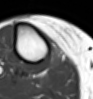
MRI of an extremity soft-tissue mass, one axial slice; MR volume resampled by the dataset authors to the PET/CT grid (not the native acquisition matrix); 3.27 mm slice thickness; 93 × 99 image matrix, field of view 91 × 97 mm. Female patient. Case-level facts recorded for this patient, not image findings: histological type: undifferentiated – high grade; grade: high; site of the primary tumour: right thigh.
Structures marked on this image (expert contour drawn on MRI and transferred to this co-registered scan by the dataset authors):
- gross tumour volume (mass): box from (x=47, y=46) to (x=62, y=69) px